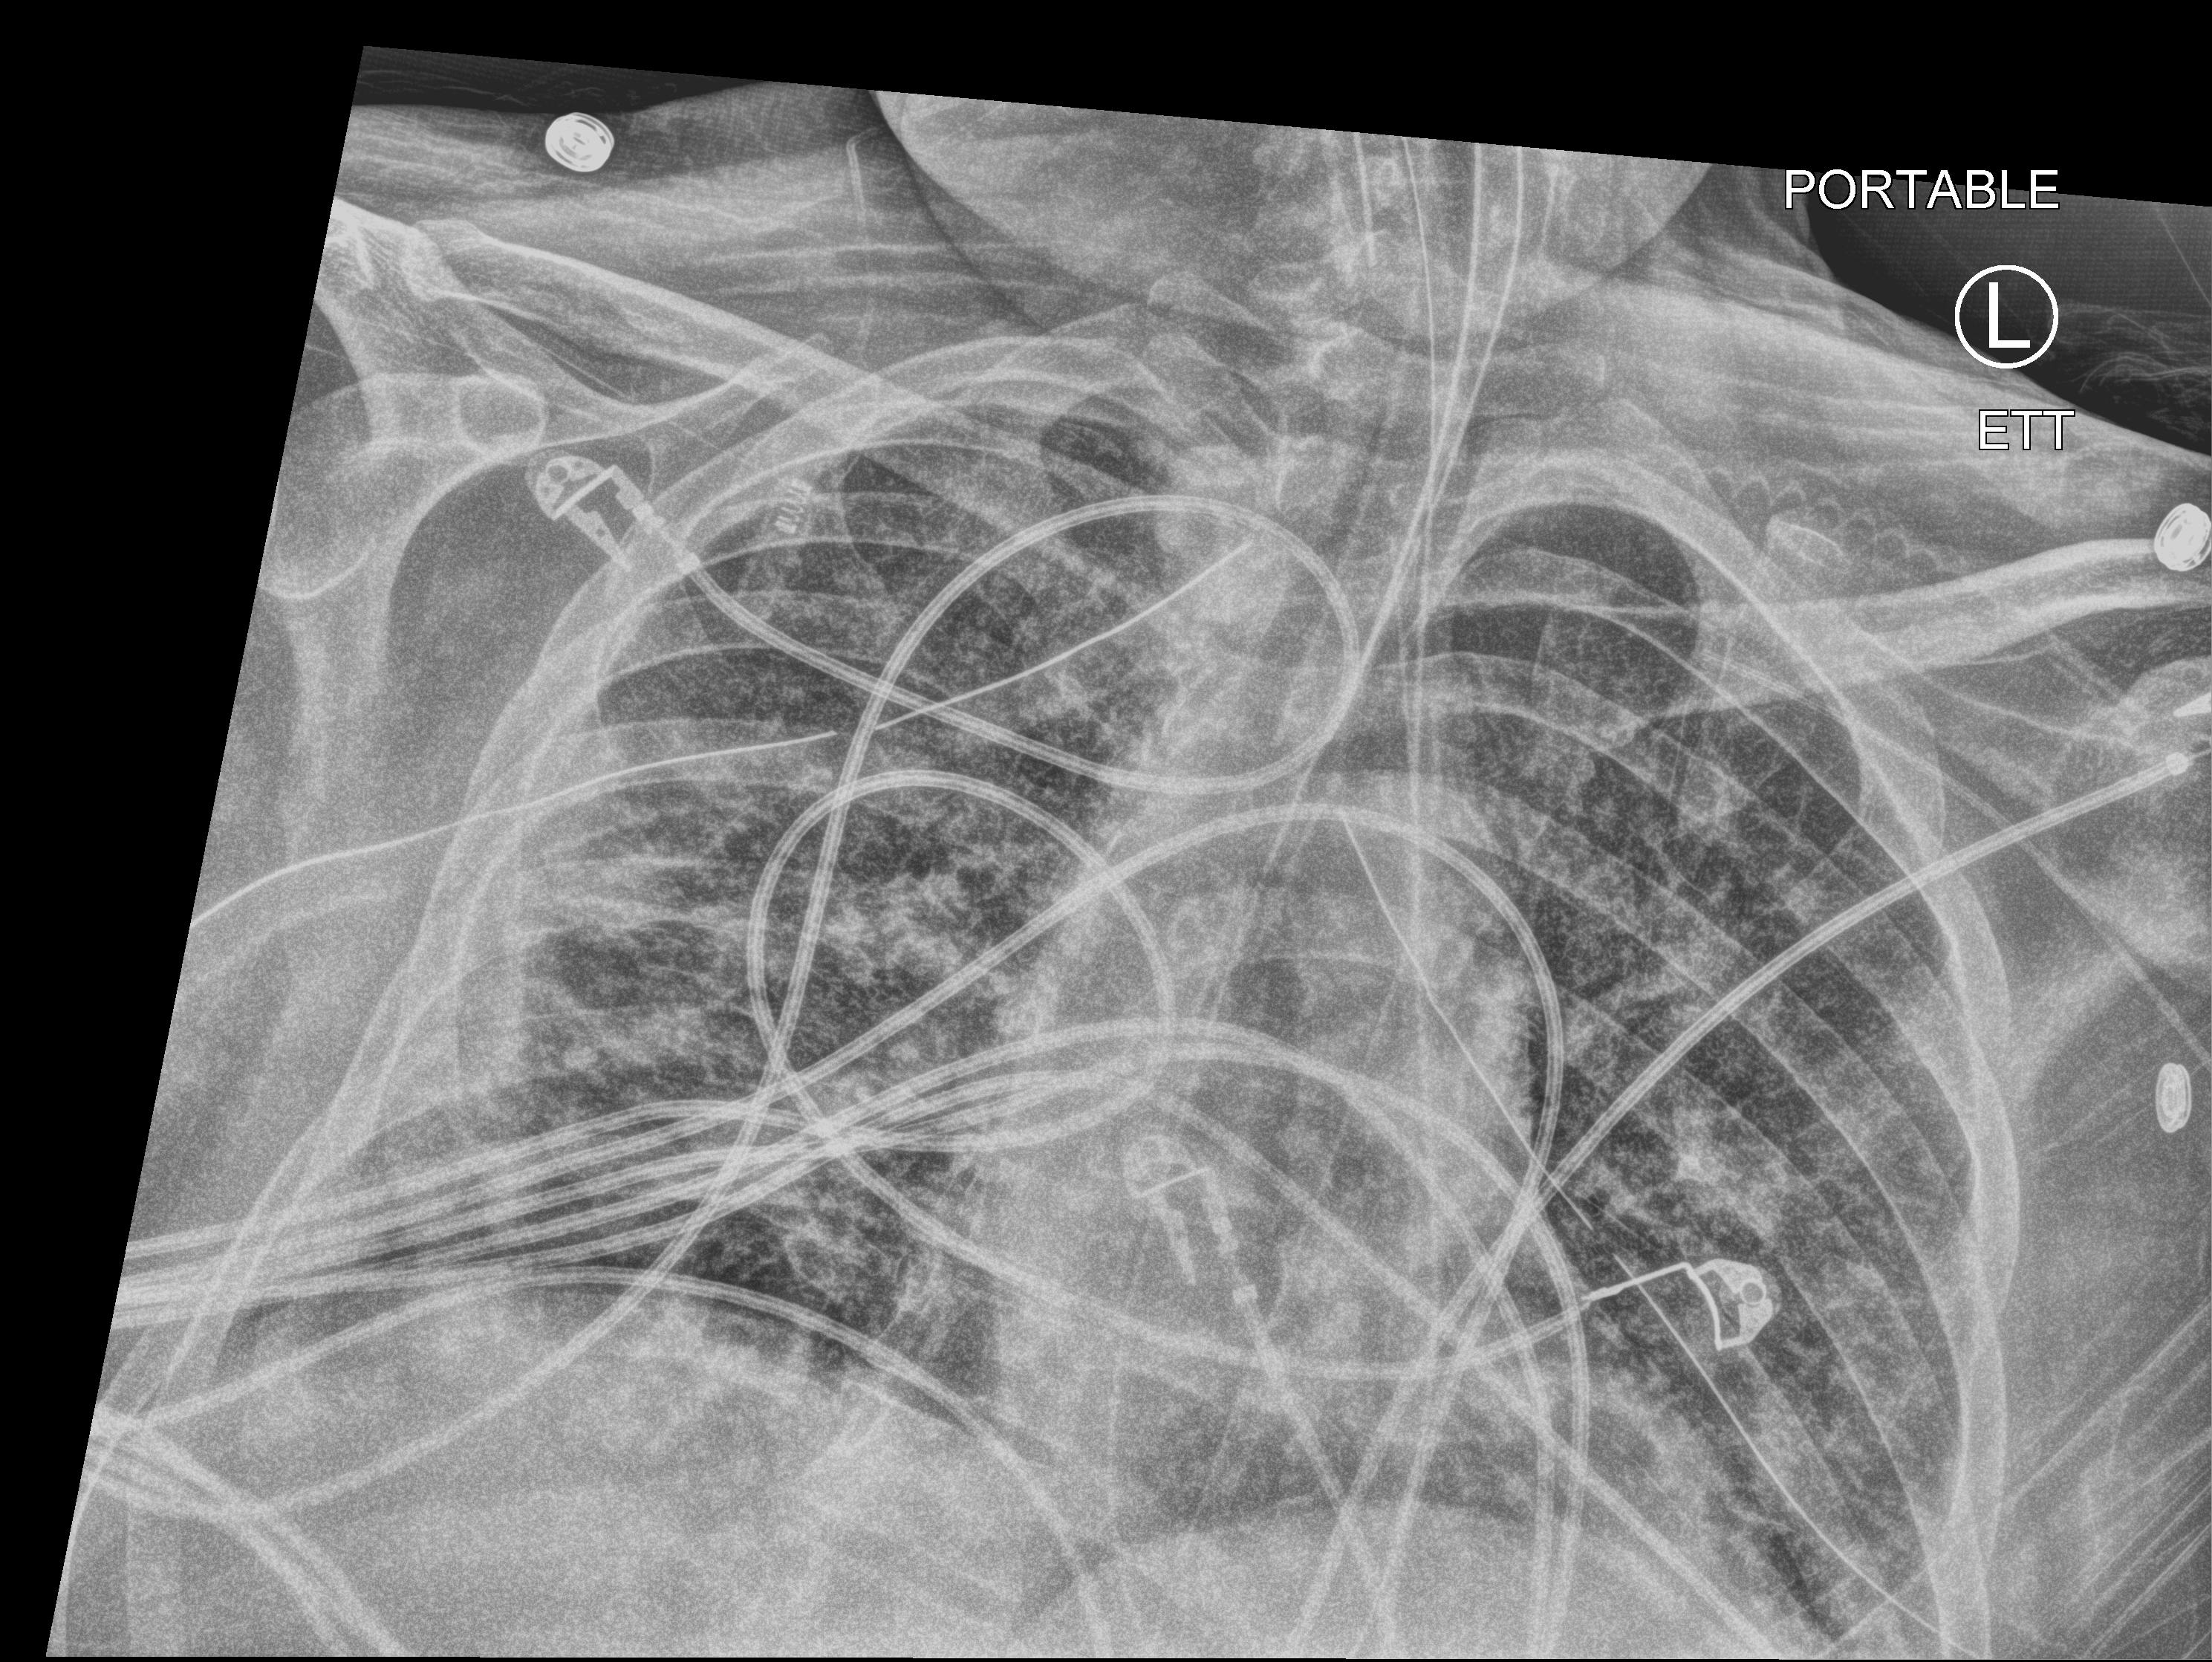
Portable chest radiograph; anteroposterior (AP) projection. Male patient hospitalised with COVID-19, age 18–59 years.
Hospital-stay facts (about this admission, not read from this image; timing relative to this image not recorded): diabetes (admission record): yes; length of hospital stay: 63 days.